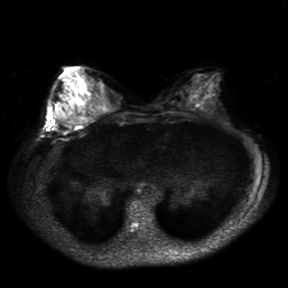
Breast MRI, one axial slice. Diffusion-weighted series; image 2 of 4 stored at this slice position (different b-values; order by instance number). 3 T. 4 mm slice thickness. 288 × 288 image matrix, field of view 360 × 360 mm. Female patient.
Structures marked on this image (outlined manually by an expert reader):
- tumour on diffusion-weighted imaging: box from (x=57, y=108) to (x=67, y=121) px